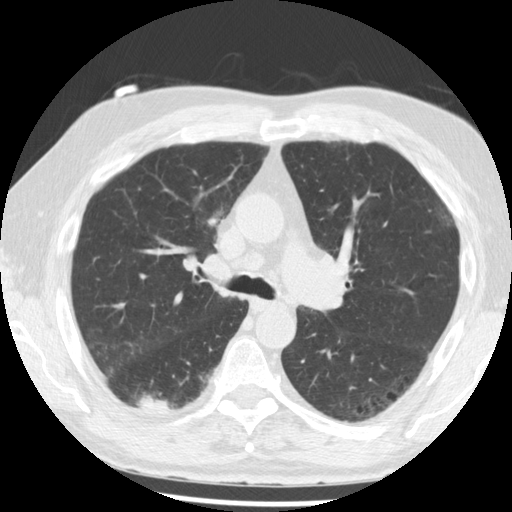
Chest CT (low-dose screening protocol), one axial image; third screening round (two years after baseline); lung window (W 1500 / L -600 HU); 2.5 mm slice thickness; 512 × 512 image matrix, field of view 350 × 350 mm. Male participant, aged 68 years at enrolment. Current smoker at enrolment.
Expert-annotated lung lesion, bounding box [x1, y1, x2, y2] px = [125, 379, 184, 424]. The screening reader recorded 3 non-calcified nodules or masses ≥4 mm on this exam (right lower lobe, right lower lobe, right lower lobe); which of them this box marks is not recorded. Later outcome: lung cancer diagnosed 48 days after this screen — squamous cell carcinoma, NOS, right lower lobe, moderately differentiated (G2), stage IB (AJCC 6th edition), 20 mm at pathology.